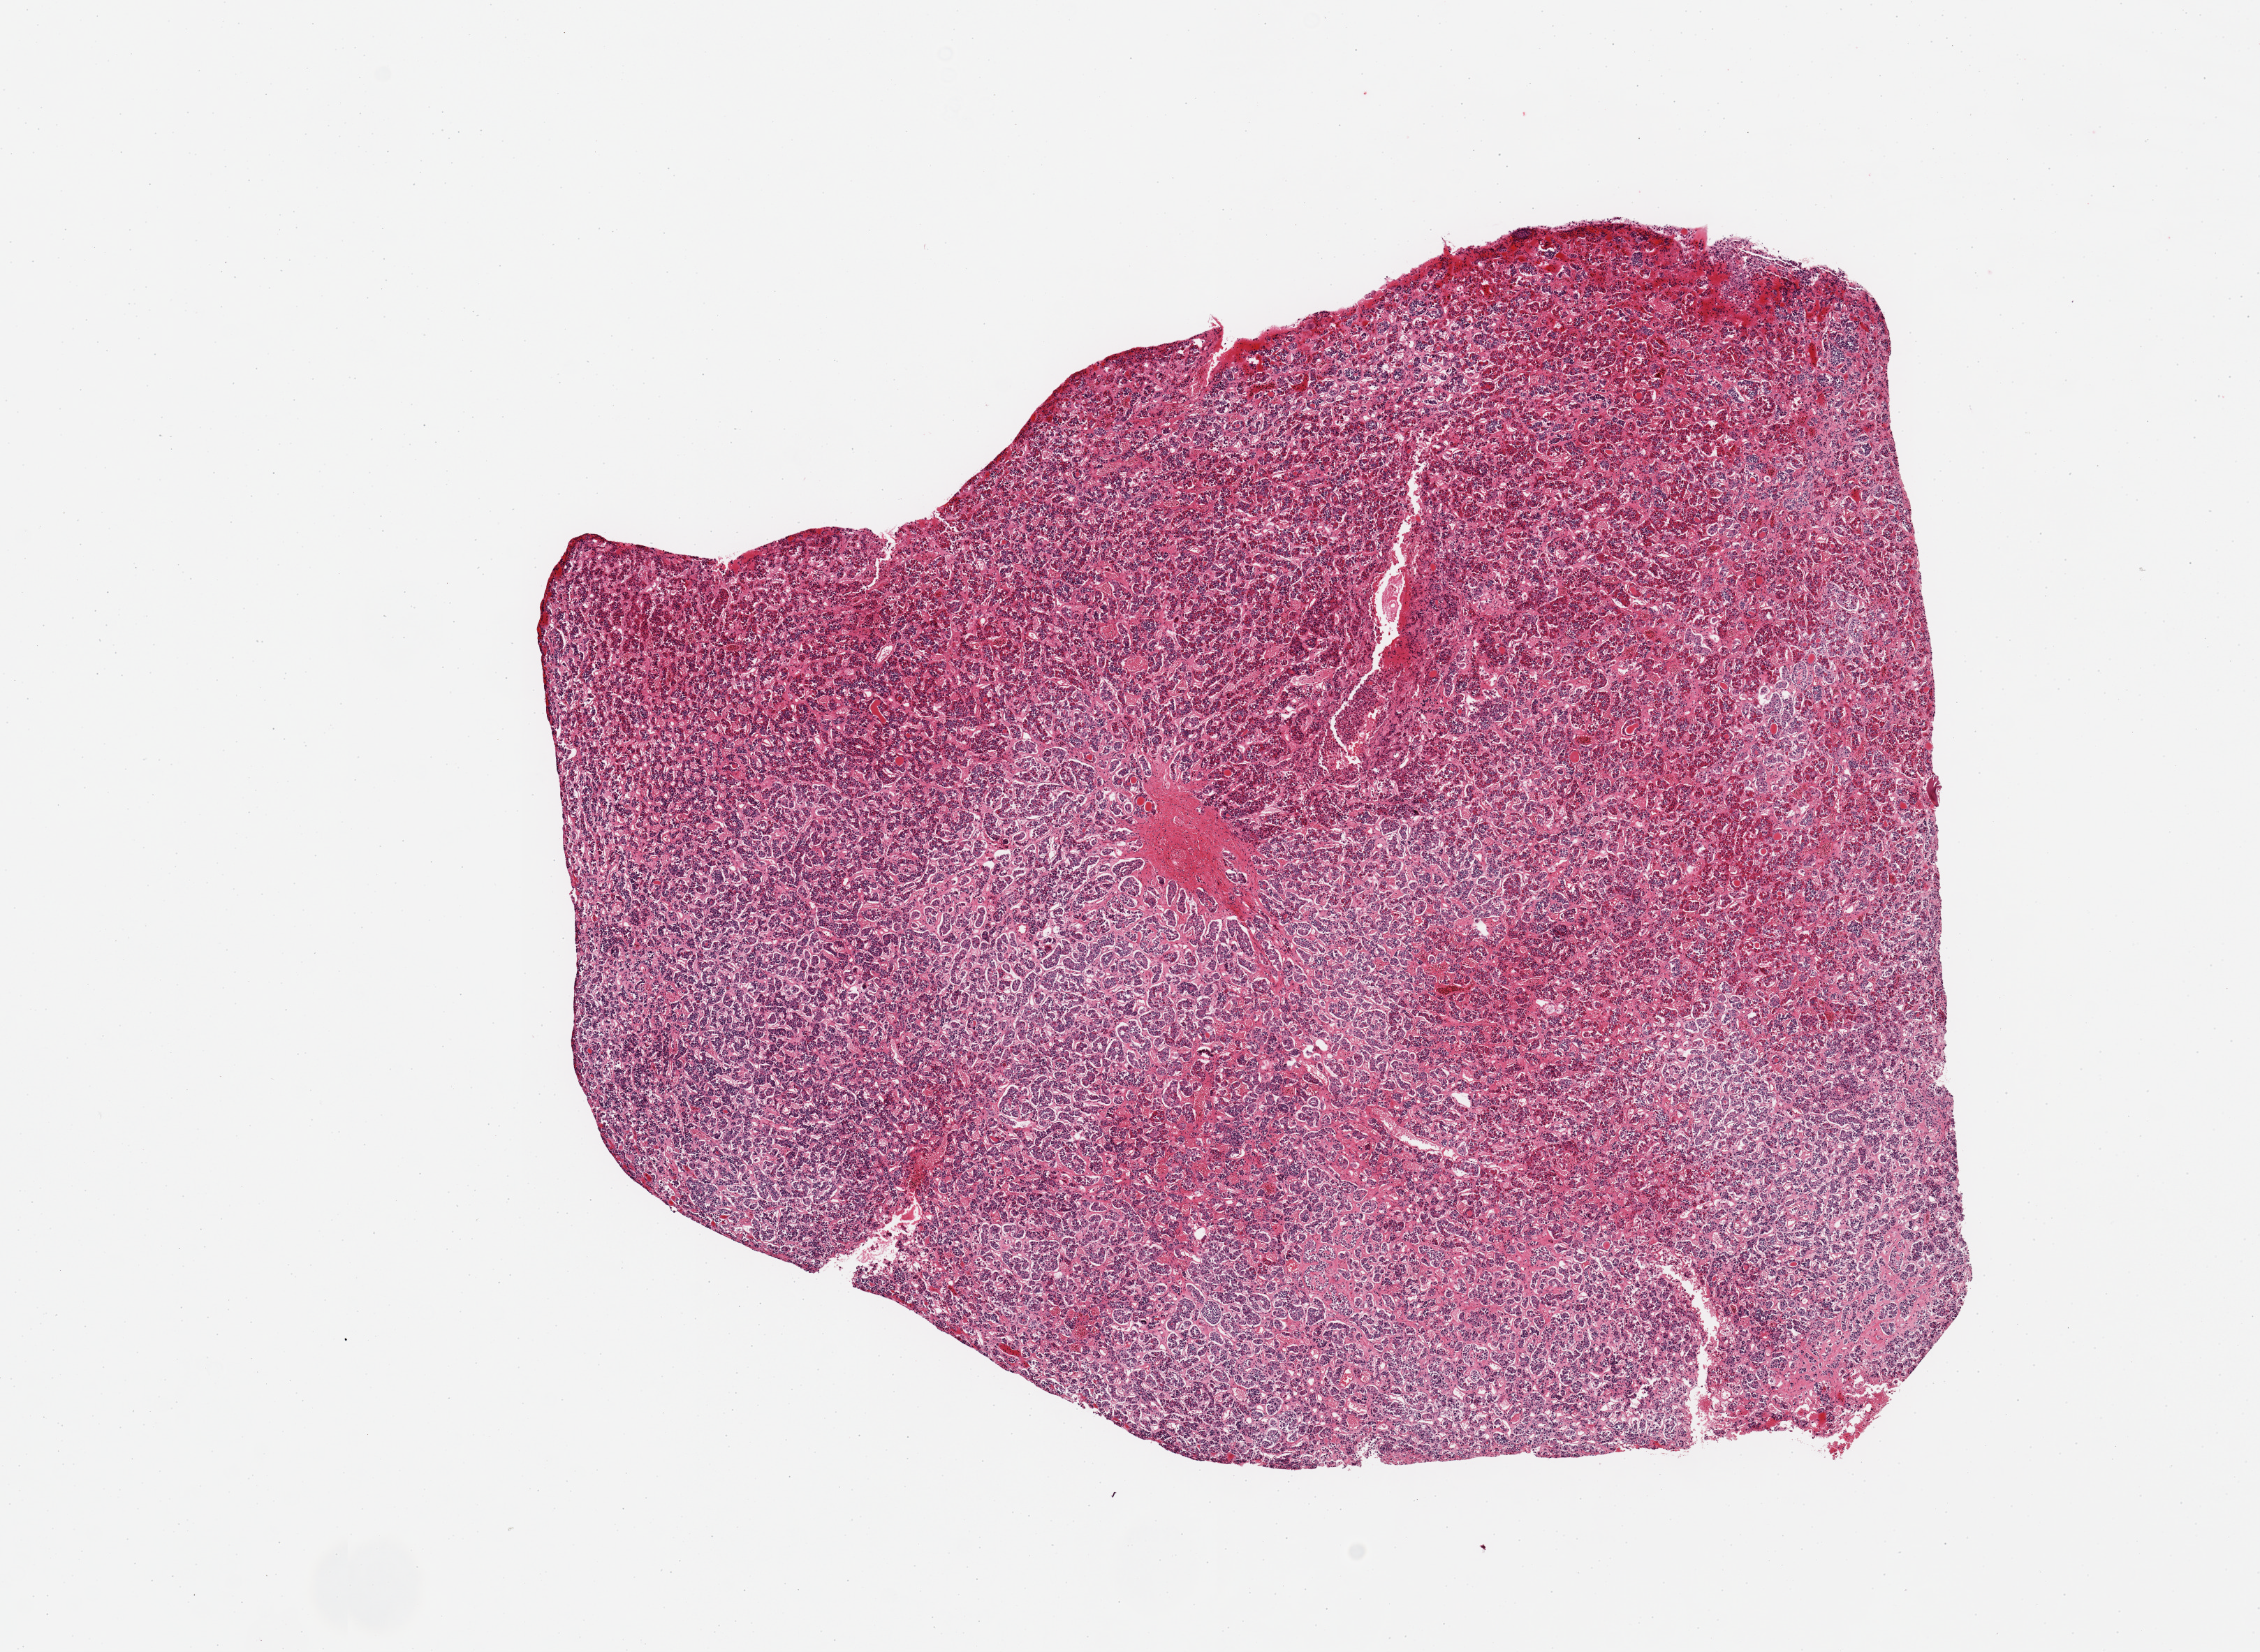
Digitized H&E-stained section, shown as a low-resolution overview of the whole scanned area (about 12.8 x 9.4 mm, from a 20x scan); PAXgene-fixed paraffin-embedded (PFPE) section; sampled site (target tissue): pituitary; tissue donor sample.
* pathologist's review note for this sample: 1 piece; all anterior portion